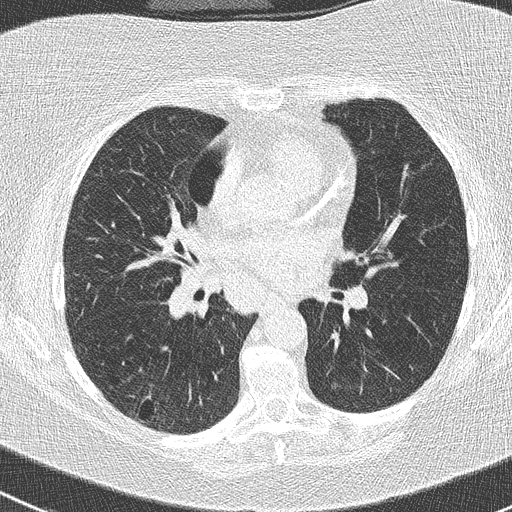
Low-dose screening chest CT, one axial slice. Slice 133 of 261 in the series (ordered by position). Lung window (W 1500 / L -600 HU). 2 mm slice thickness. 512 × 512 image matrix, field of view 310 × 310 mm.
Outlined on this slice (expert manual segmentation):
- lesion 1 (tumor, lower lobe of right lung): bounding box <148,396,150,398> (left, top, right, bottom; pixels)